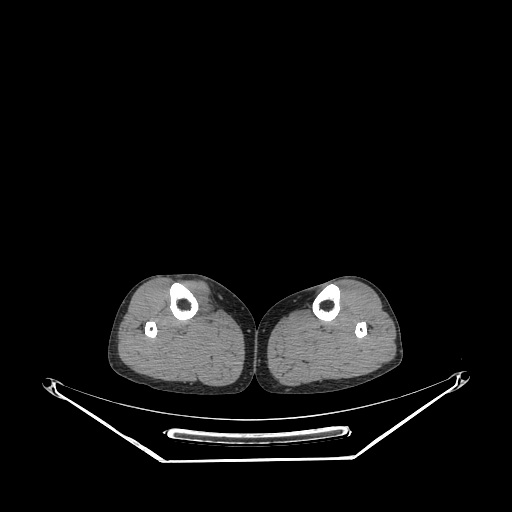
CT of an extremity soft-tissue mass (from a PET/CT study), one axial slice; position 140 of 267 along the scan axis; reconstruction kernel STANDARD; 140 kVp; soft-tissue window (W 400 / L 40 HU); 3.75 mm slice thickness; 512 × 512 image matrix. Female patient. Case-level facts recorded for this patient, not image findings: histological type: undifferentiated – high grade; grade: high; site of the primary tumour: right thigh.
Structures marked on this image (expert contour drawn on MRI and transferred to this co-registered scan by the dataset authors):
- gross tumour volume (mass): box from (x=183, y=283) to (x=211, y=314) px